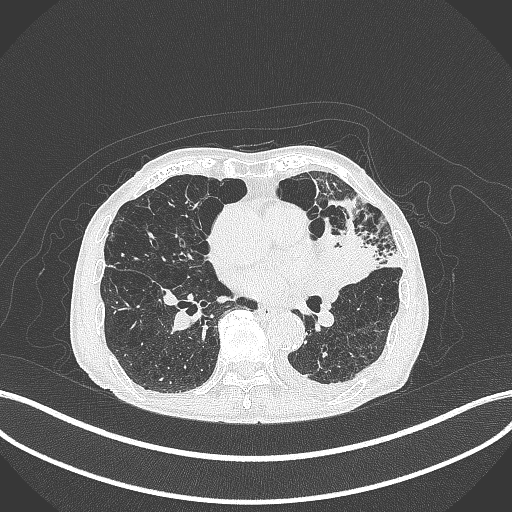
Chest CT, one axial slice; slice 177 of 385 in the series (ordered by position); 120 kVp; lung window (W 1500 / L -600 HU); 1 mm slice thickness; 512 × 512 image matrix, field of view 400 × 400 mm. Patient: male, 90 years or older. Case-level facts recorded for this patient, not image findings: clinical TNM (as recorded): T2b N1 M0.
Structures marked on this image (bounding box drawn by a radiologist):
- lung tumour (recorded histology: squamous cell carcinoma): bounding box [x1, y1, x2, y2] px = [312, 228, 374, 283]